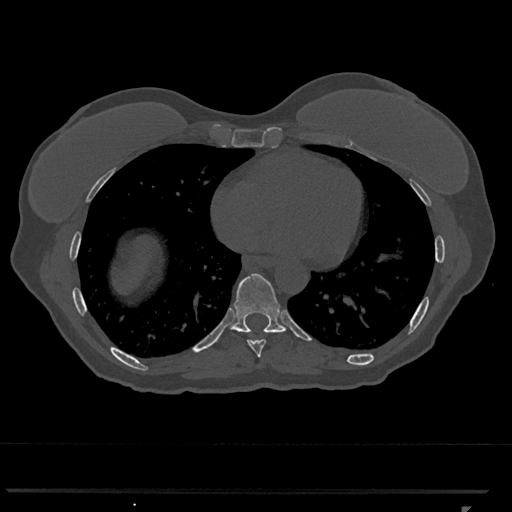
CT including the spine, one axial slice; position 638 of 793 along the scan axis; reconstruction kernel Br40s/3; 120 kVp; bone window (W 1800 / L 400 HU); 512 × 512 image matrix, field of view 380 × 380 mm. Female patient, age 62 years. Case-level facts recorded for this patient, not image findings: primary cancer: renal.
Outlined on this slice (semi-automatically segmented with operator editing):
- T8 vertebra: bounding box [x1, y1, x2, y2] px = [247, 339, 266, 358]
- T9 vertebra: [230, 273, 286, 333]